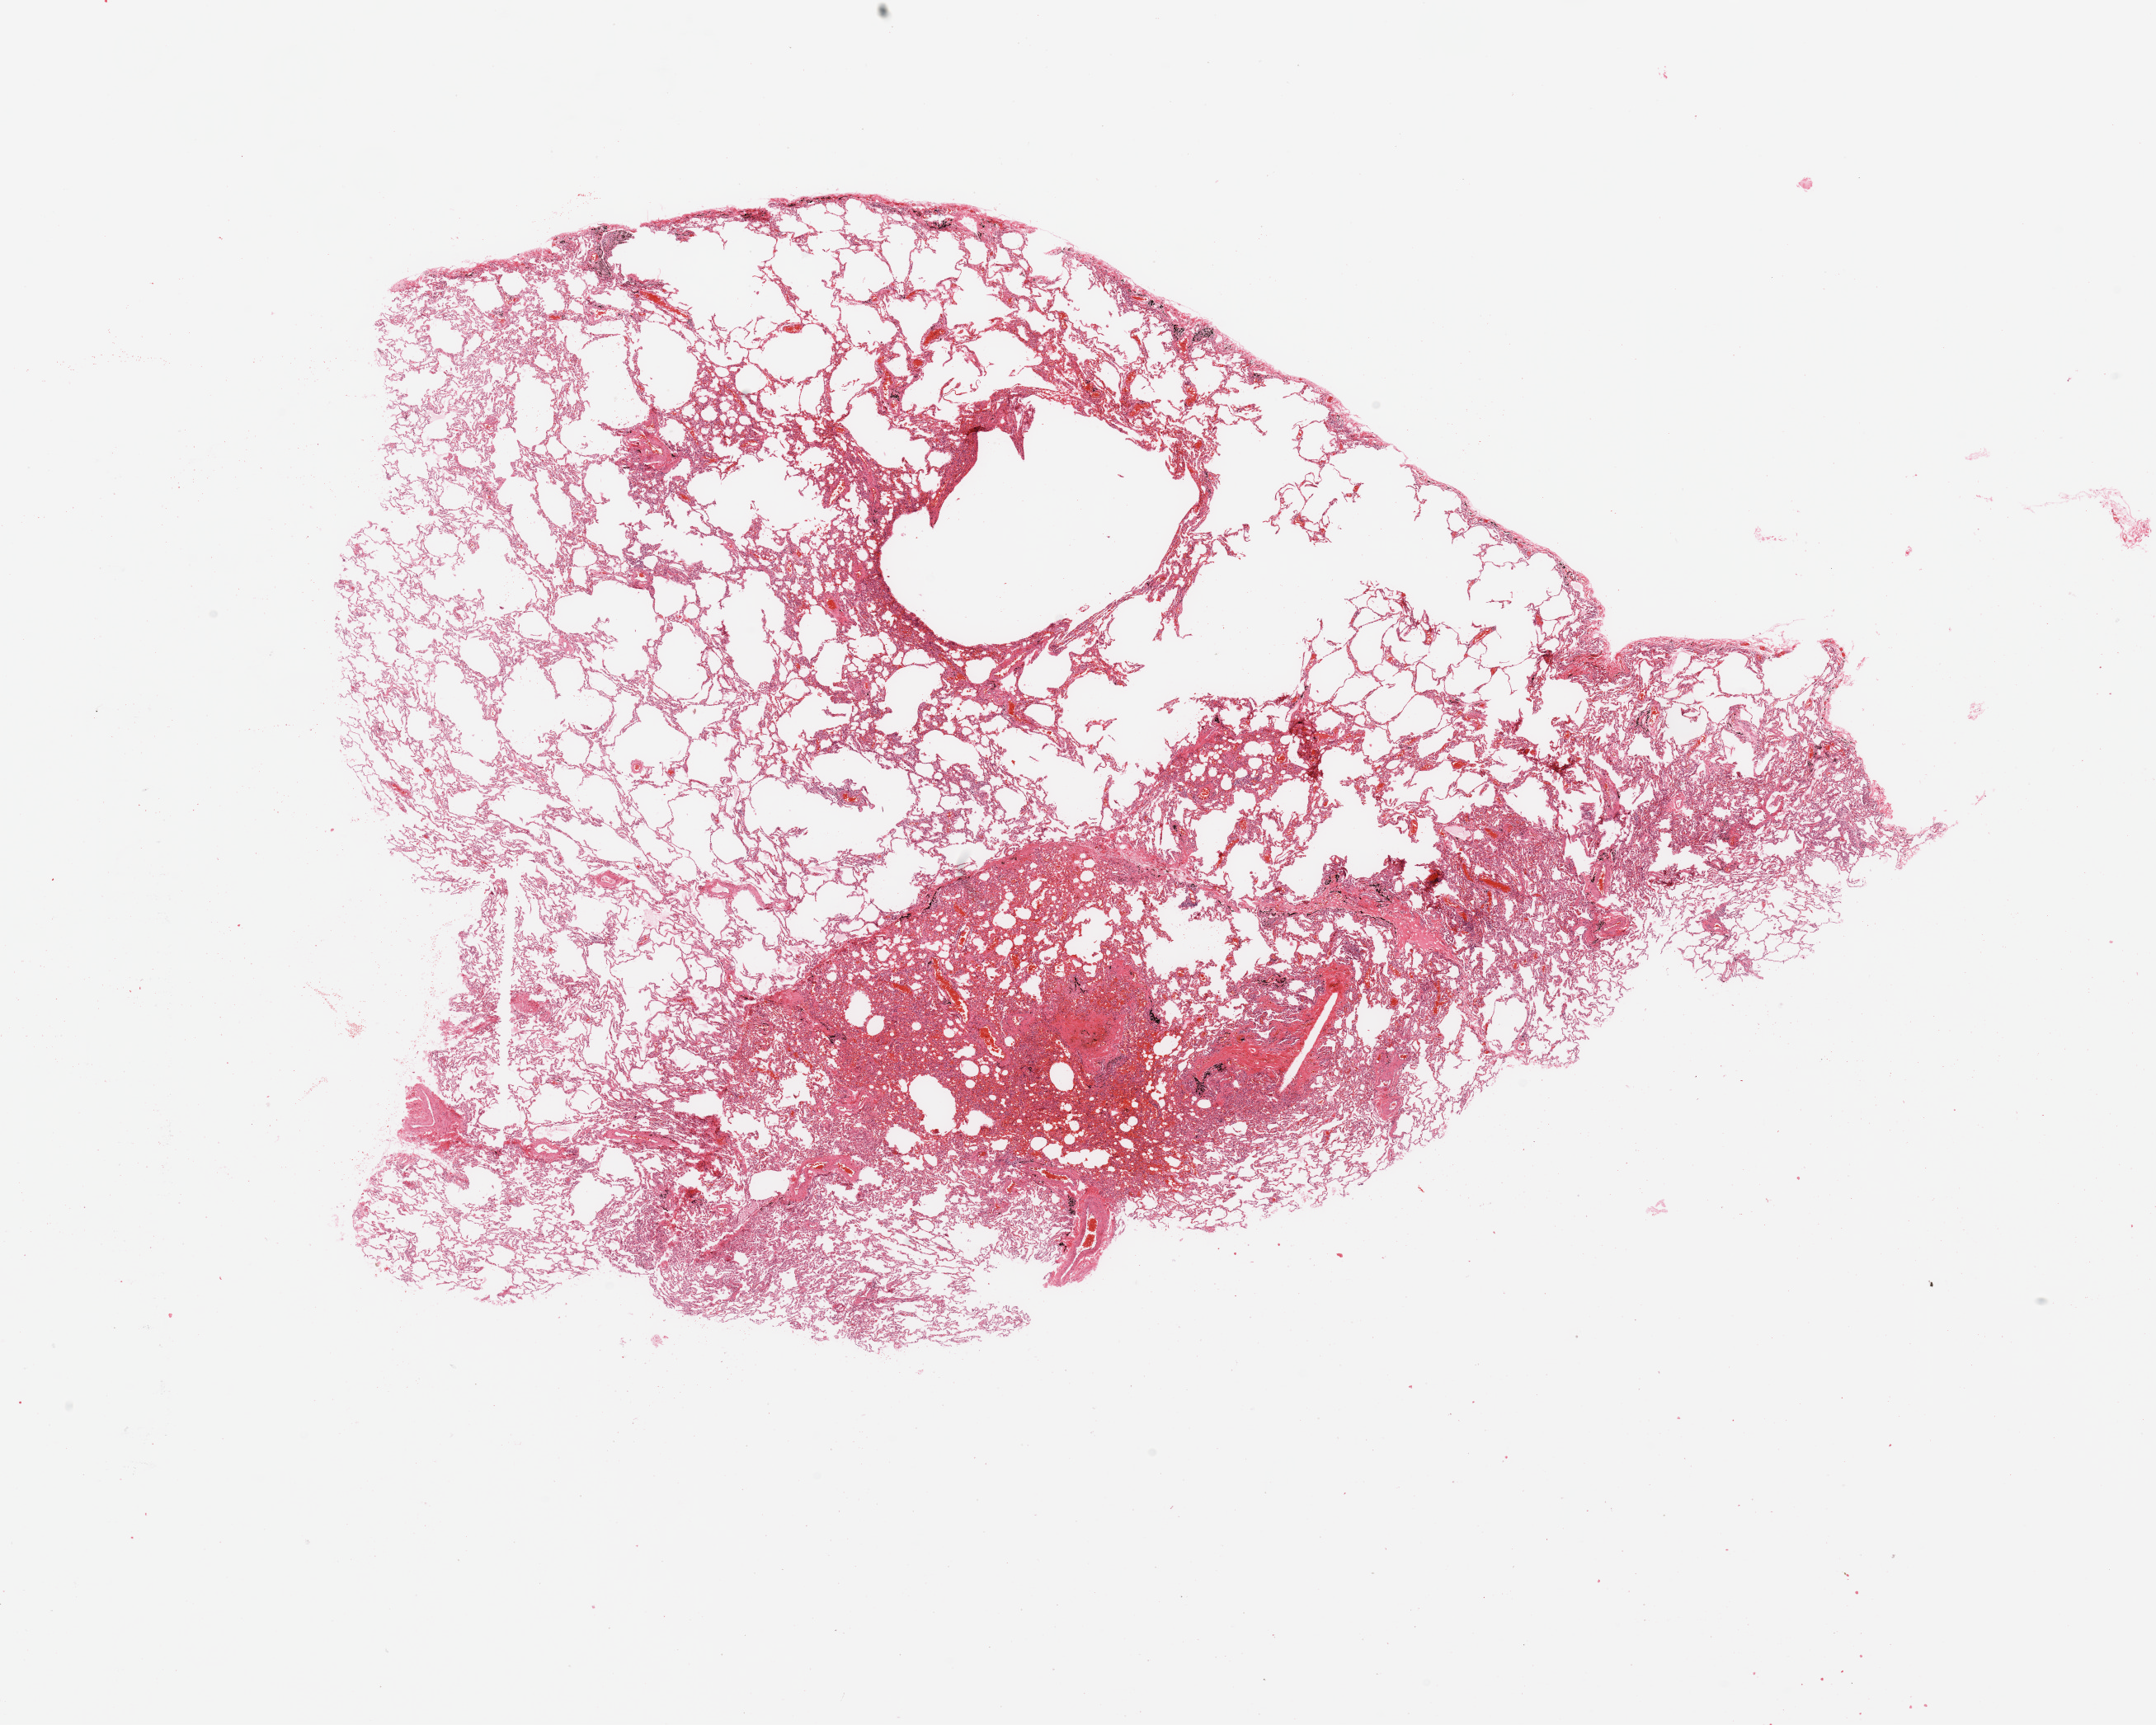
Whole-slide histology image, H&E-stained, whole scanned area (about 20.7 x 16.5 mm, slide scanned at 20x) shown as a low-resolution overview, lung, normal (non-tumour) tissue. Patient: male, age 67 years.
This section: normal (non-tumour) tissue from the same patient. Patient diagnosis: Adenocarcinoma, NOS.